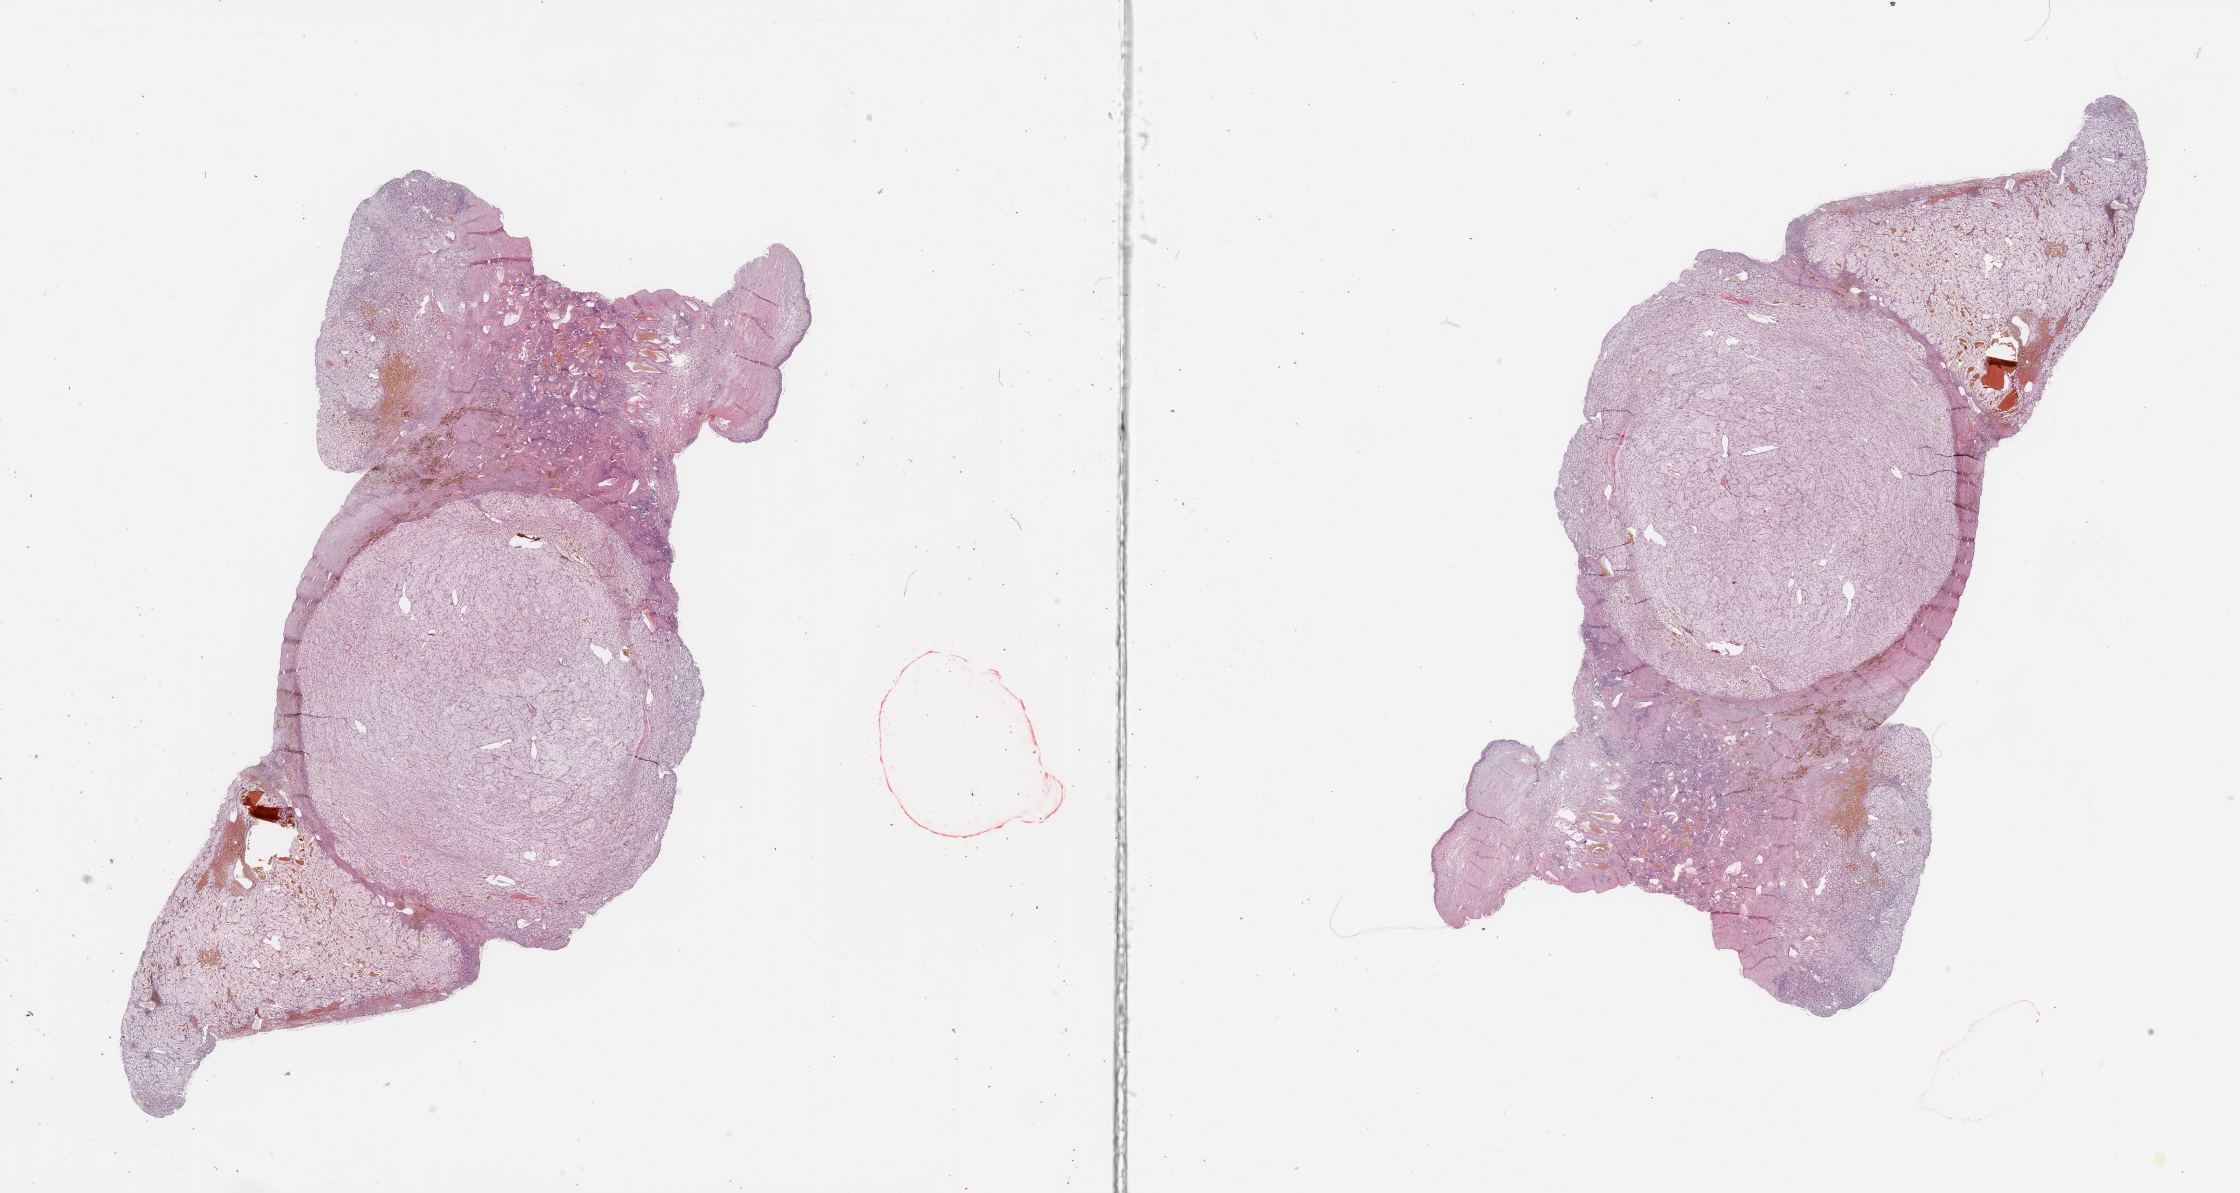
Whole-slide histology image, Hematoxylin and eosin (H&E) stained, low-resolution overview of the scanned area, about 35.4 x 18.9 mm (acquisition: 20x scan), tumour tissue sample, sampled site: kidney. 53-year-old male patient. Histologic grade: G3 (poorly differentiated). Composition of this section per pathologist review: tumour nuclei 85%, necrosis 0%.
AJCC pathologic stage: IV. Diagnosis: Renal cell carcinoma, NOS. Primary tumour site (as recorded): upper pole.